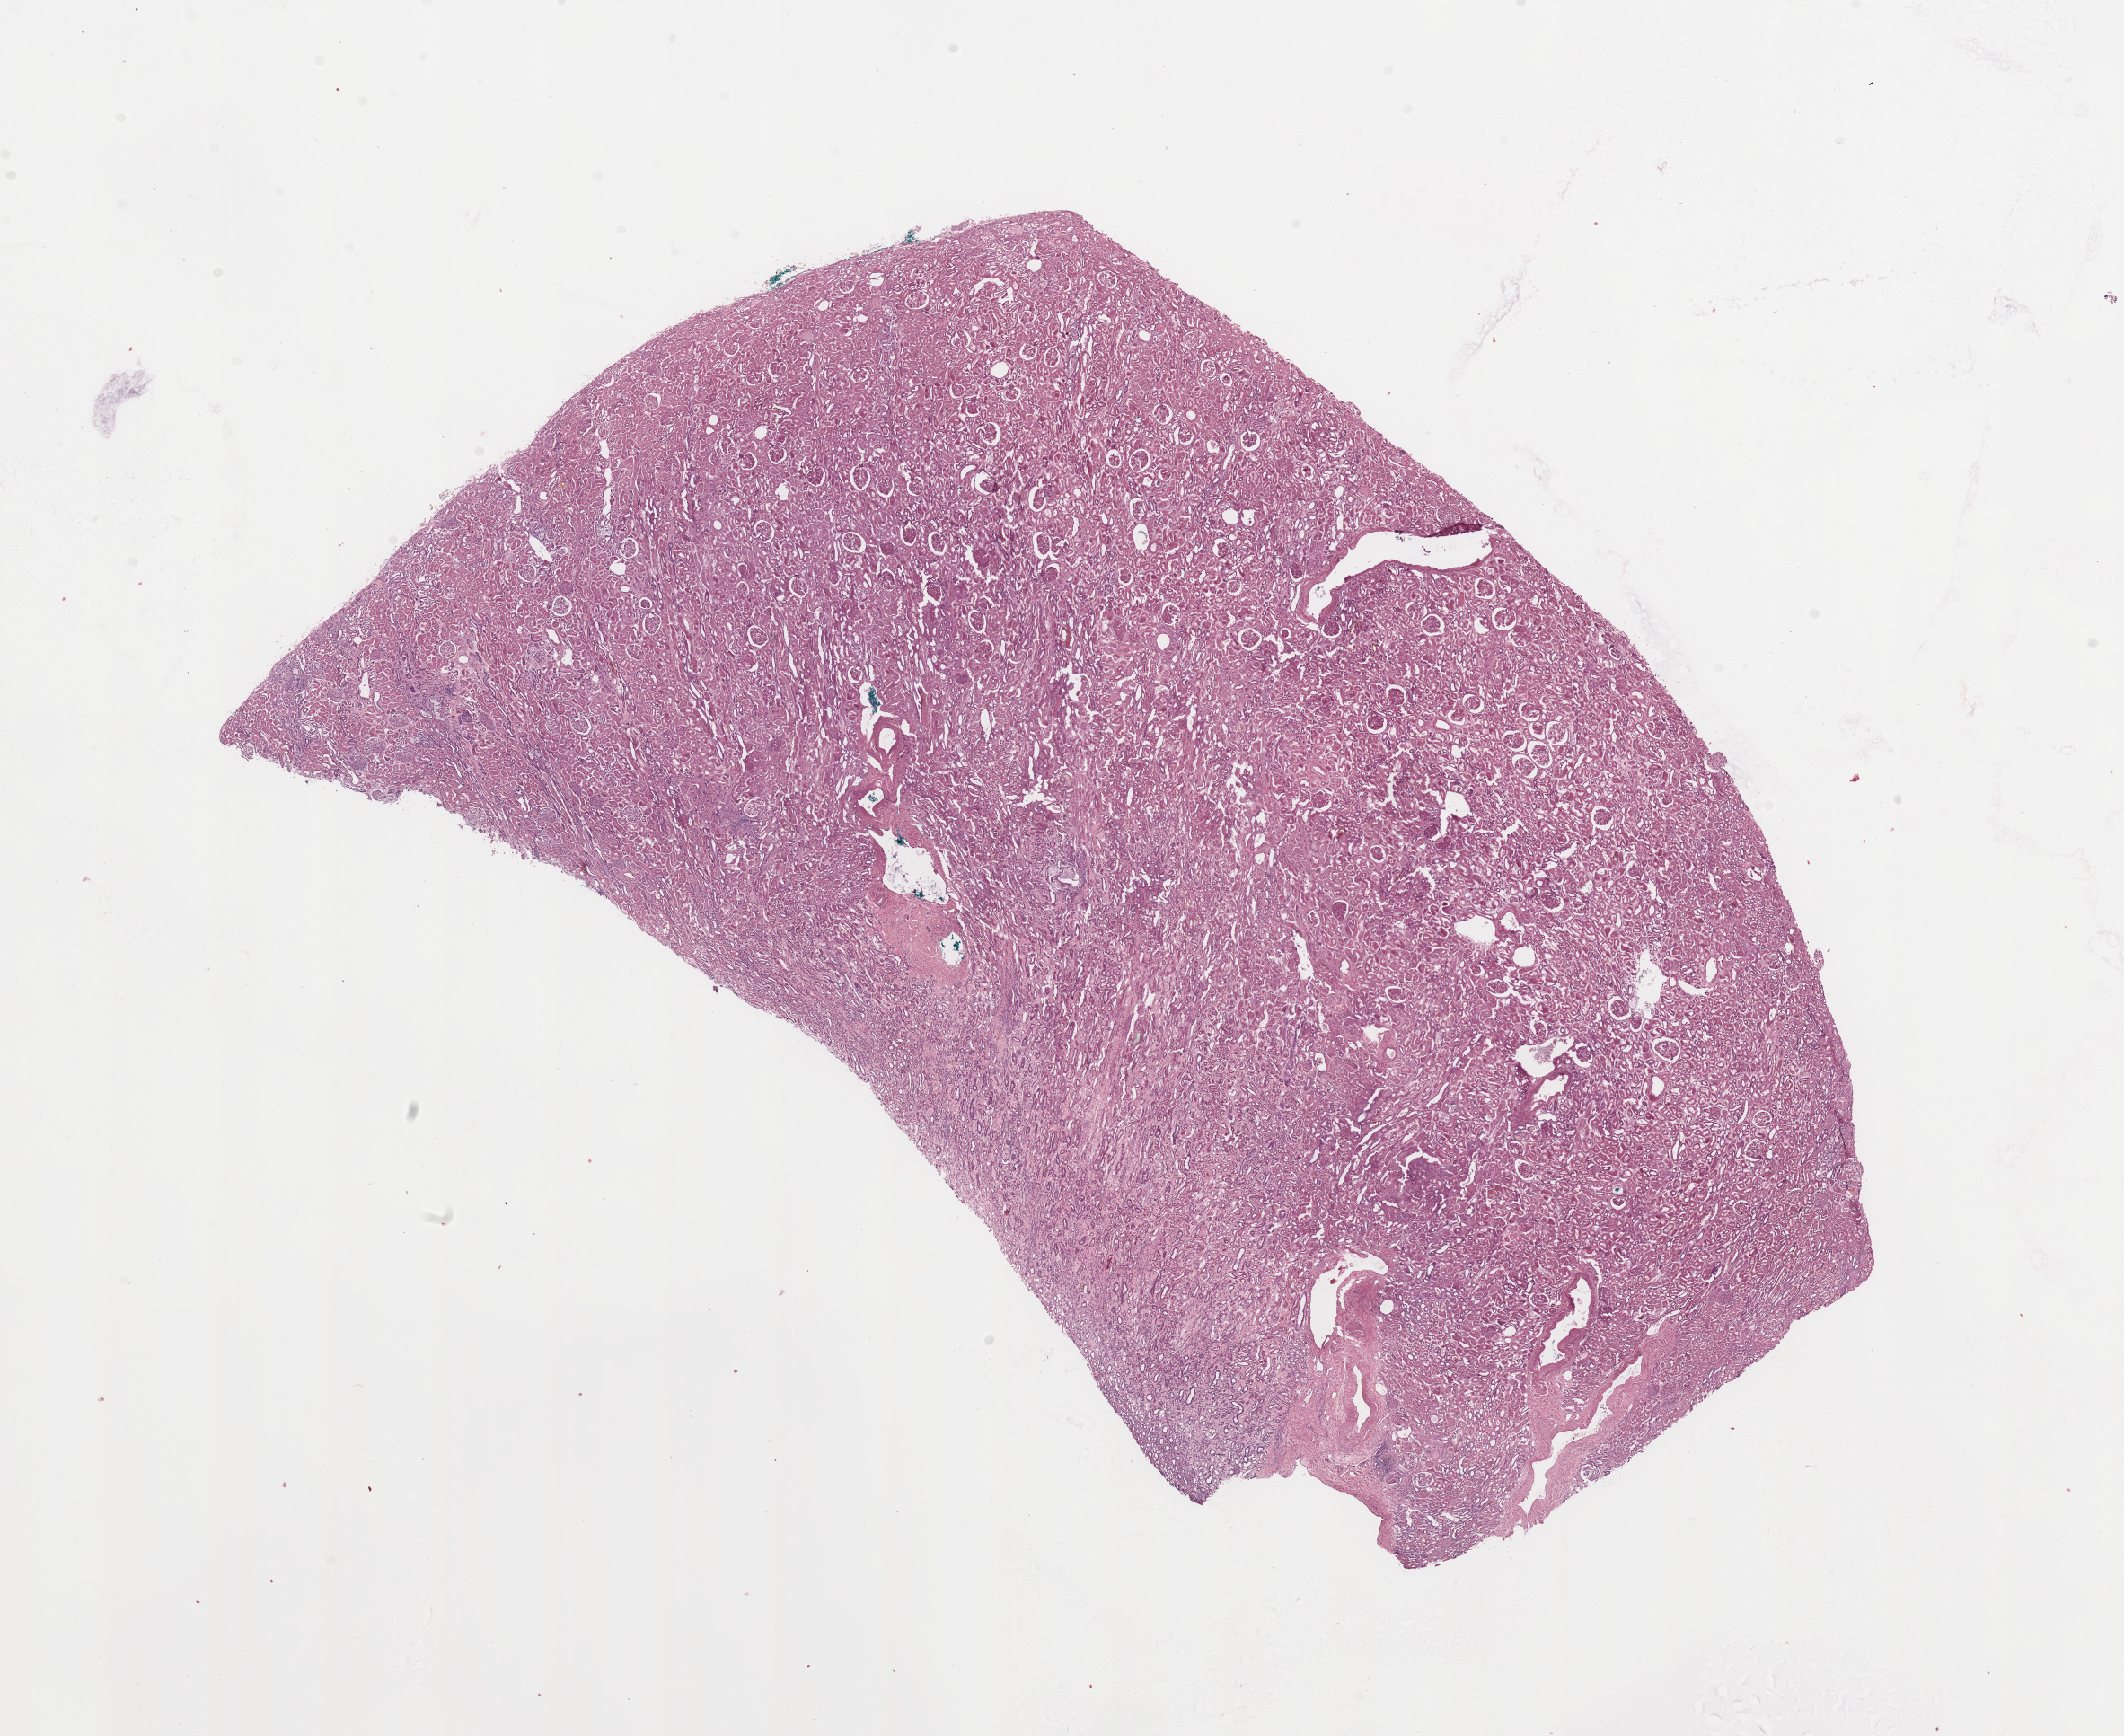
Whole-slide histology image, H&E-stained, shown as a low-resolution overview of the whole scanned area (about 18.7 x 15.3 mm, from a 20x scan); normal (non-tumour) tissue sample, sampled site: kidney. 45-year-old male patient.
* this section: normal (non-tumour) tissue from the same patient
* patient diagnosis: Renal cell carcinoma, NOS